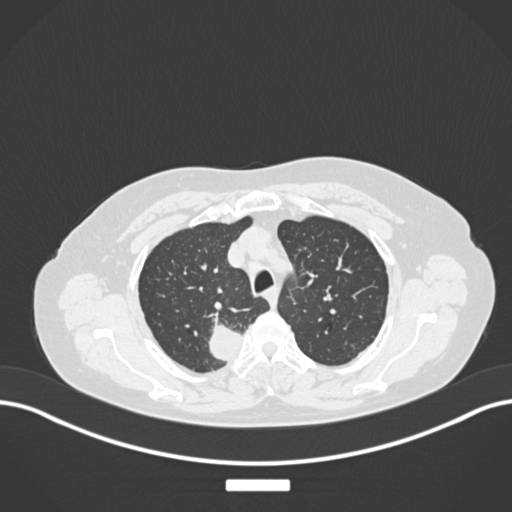
Chest CT, one axial slice; slice 205 of 237 in the series (ordered by position); reconstruction kernel B30f; lung window (W 1500 / L -600 HU); 1 mm slice thickness; 512 × 512 image matrix. Patient: female, 62 years. Case-level facts recorded for this patient, not image findings: clinical TNM (as recorded): T1c N1 M0.
Structures marked on this image (bounding box drawn by a radiologist):
- lung tumour (recorded histology: squamous cell carcinoma): bounding box [x1, y1, x2, y2] px = [201, 321, 244, 368]